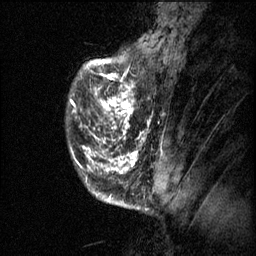
Breast MRI (dynamic contrast-enhanced), one sagittal slice. Slice 12 of 60 in the series (ordered by position). 3 images stored at this slice position (order not interpretable as contrast timing). 1.5 T. TE 4.2 ms, TR 11.1 ms. 256 × 256 image matrix, field of view 180 × 180 mm. Female patient, age 50 years.
Outlined on this slice (semi-automatic segmentation, software-assisted and operator-edited):
- analysis volume of interest (the breast-tissue region the enhancement analysis was run in; not a lesion): bounding box [x1, y1, x2, y2] px = [68, 68, 153, 141]
- tumour enhancement mask (voxels above the 70 % enhancement threshold inside the analysis volume of interest): [71, 68, 150, 141]